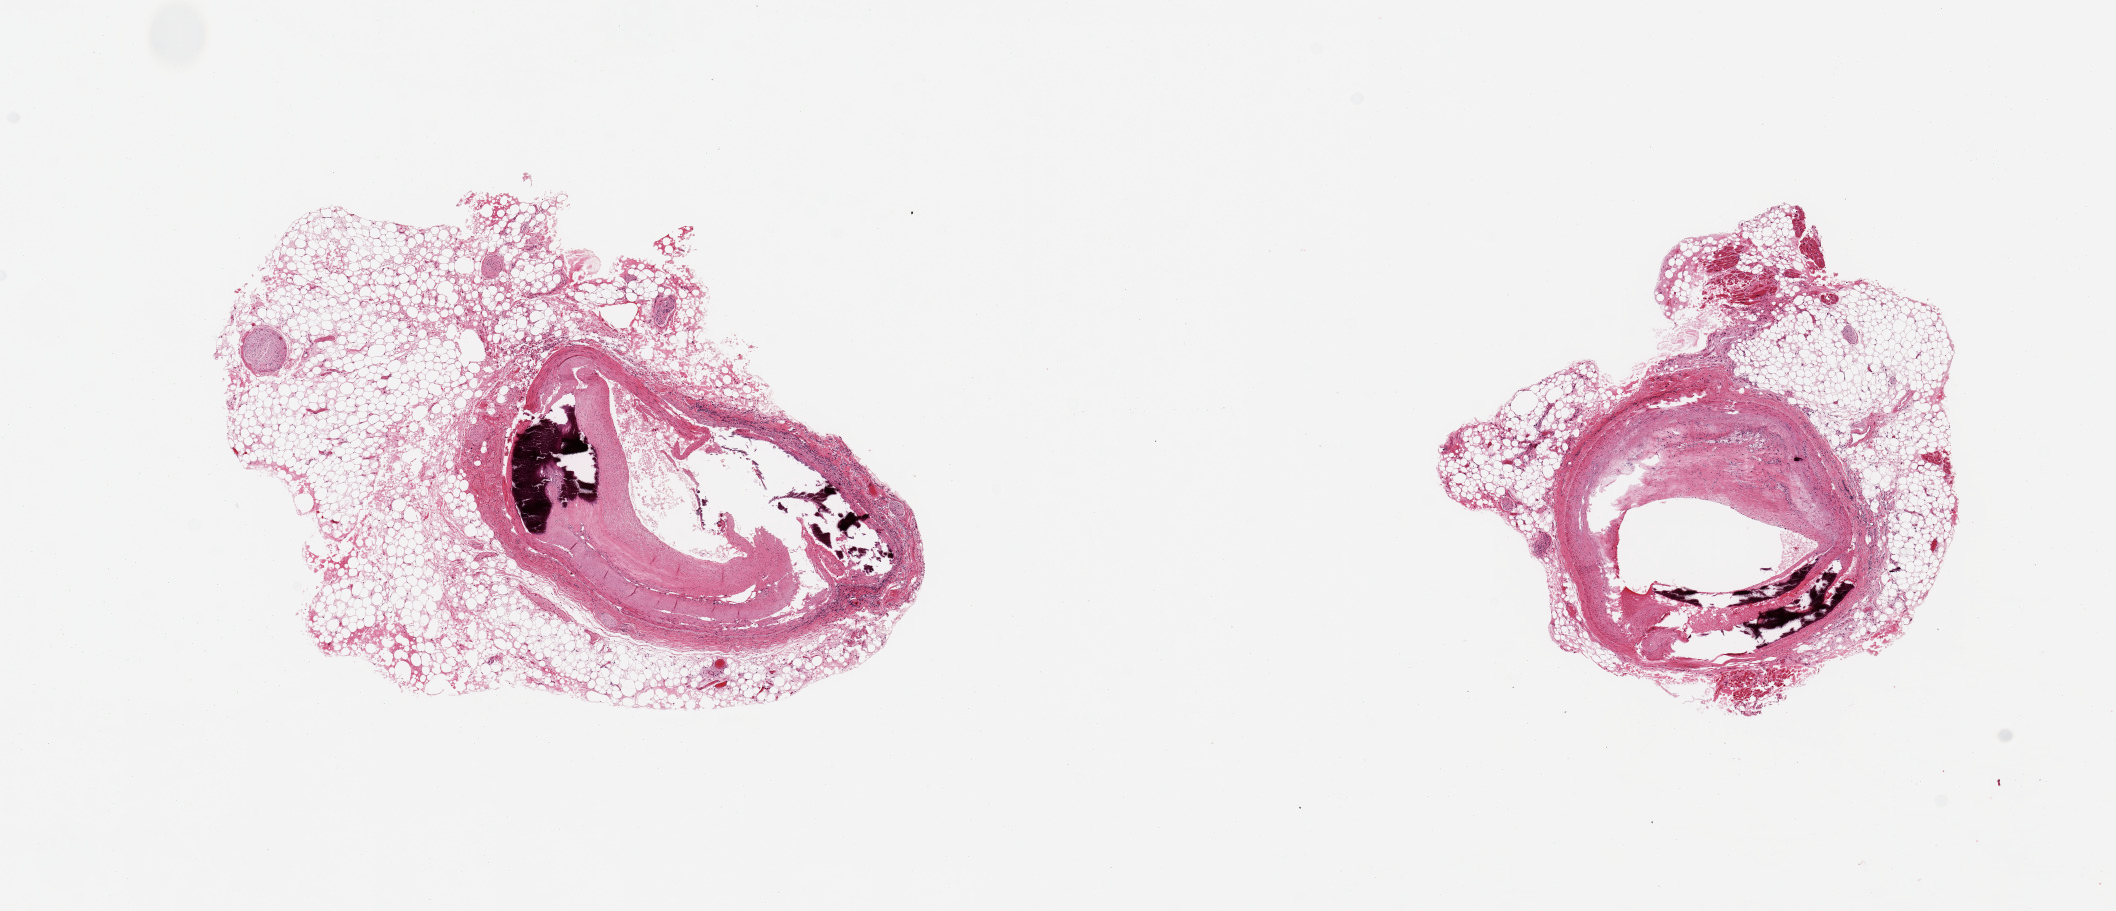
Digitized hematoxylin and eosin (H&E)-stained section, brightfield, whole scanned area (about 16.7 x 7.2 mm, slide scanned at 20x) shown as a low-resolution overview; PAXgene-fixed paraffin-embedded (PFPE) section; target tissue: coronary artery; tissue donor sample. Donor sex: female.
- review note (as recorded): 2 ~2.5mm d aliquots, both with 40-50% adherent fat peripherally, layer of up to 1.5-2mm. 60-70% occlusive atherosclerotic deposits, focally calcified